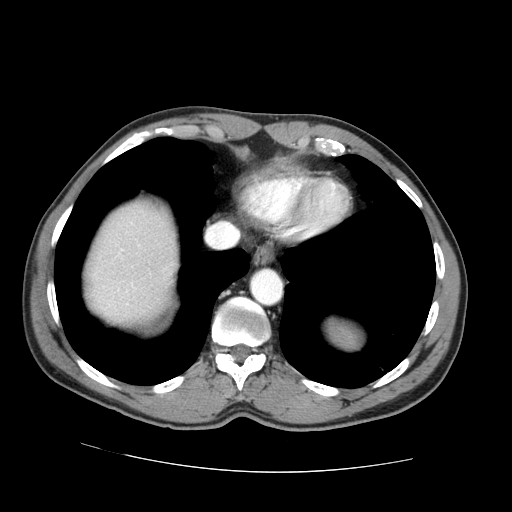
Contrast-enhanced abdominal CT (liver protocol), one axial slice. Slice 64 of 73 in the series (ordered by position). Reconstruction kernel STANDARD. 100 kVp. One of 2 acquisitions stored at this slice position. Soft-tissue window (W 400 / L 40 HU). 512 × 512 image matrix, field of view 380 × 380 mm. Case-level facts recorded for this patient, not image findings: diagnosis: hepatocellular carcinoma (patient treated with transarterial chemoembolisation; whether this scan precedes or follows treatment is not stated here); TNM stage (as recorded): Stage-IVA; Child-Pugh class: A; tumour differentiation: no biopsy.
Outlined on this slice (semi-automatic segmentation, software-assisted and operator-edited):
- abdominal aorta: bounding box [x1, y1, x2, y2] px = [252, 270, 281, 303]
- liver parenchyma outside the tumour (the mass and vessels are separate outlines, so this box may not span the whole liver): [86, 204, 176, 322]